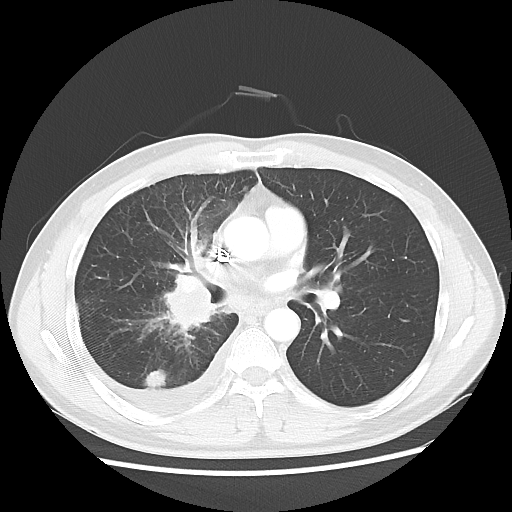
Chest CT, one axial slice. Position 29 of 56 along the scan axis. Reconstruction kernel LUNG. 120 kVp. Lung window (W 1500 / L -600 HU). 5 mm slice thickness. 512 × 512 image matrix. Male patient, age 46 years. Case-level facts recorded for this patient, not image findings: clinical TNM (as recorded): T2 N3 M1.
Structures marked on this image (rectangle marked by the reading radiologist):
- lung tumour (recorded histology: adenocarcinoma): bounding box [x1, y1, x2, y2] px = [153, 250, 223, 342]